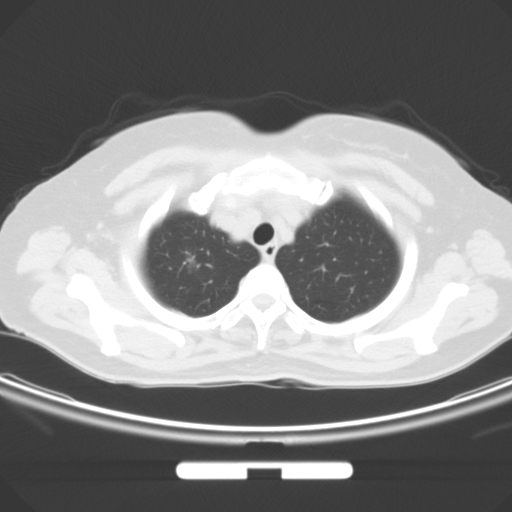
Chest CT, one axial slice; position 51 of 59 along the scan axis; 120 kVp; lung window (W 1500 / L -600 HU); 512 × 512 image matrix, field of view 369 × 369 mm. Patient: female, 58 years. From the clinical record (not read from this slice): clinical TNM (as recorded): T1b N0 M0.
Outlined on this slice (rectangle marked by the reading radiologist):
- lung tumour (recorded histology: adenocarcinoma): box from (x=179, y=249) to (x=202, y=274) px